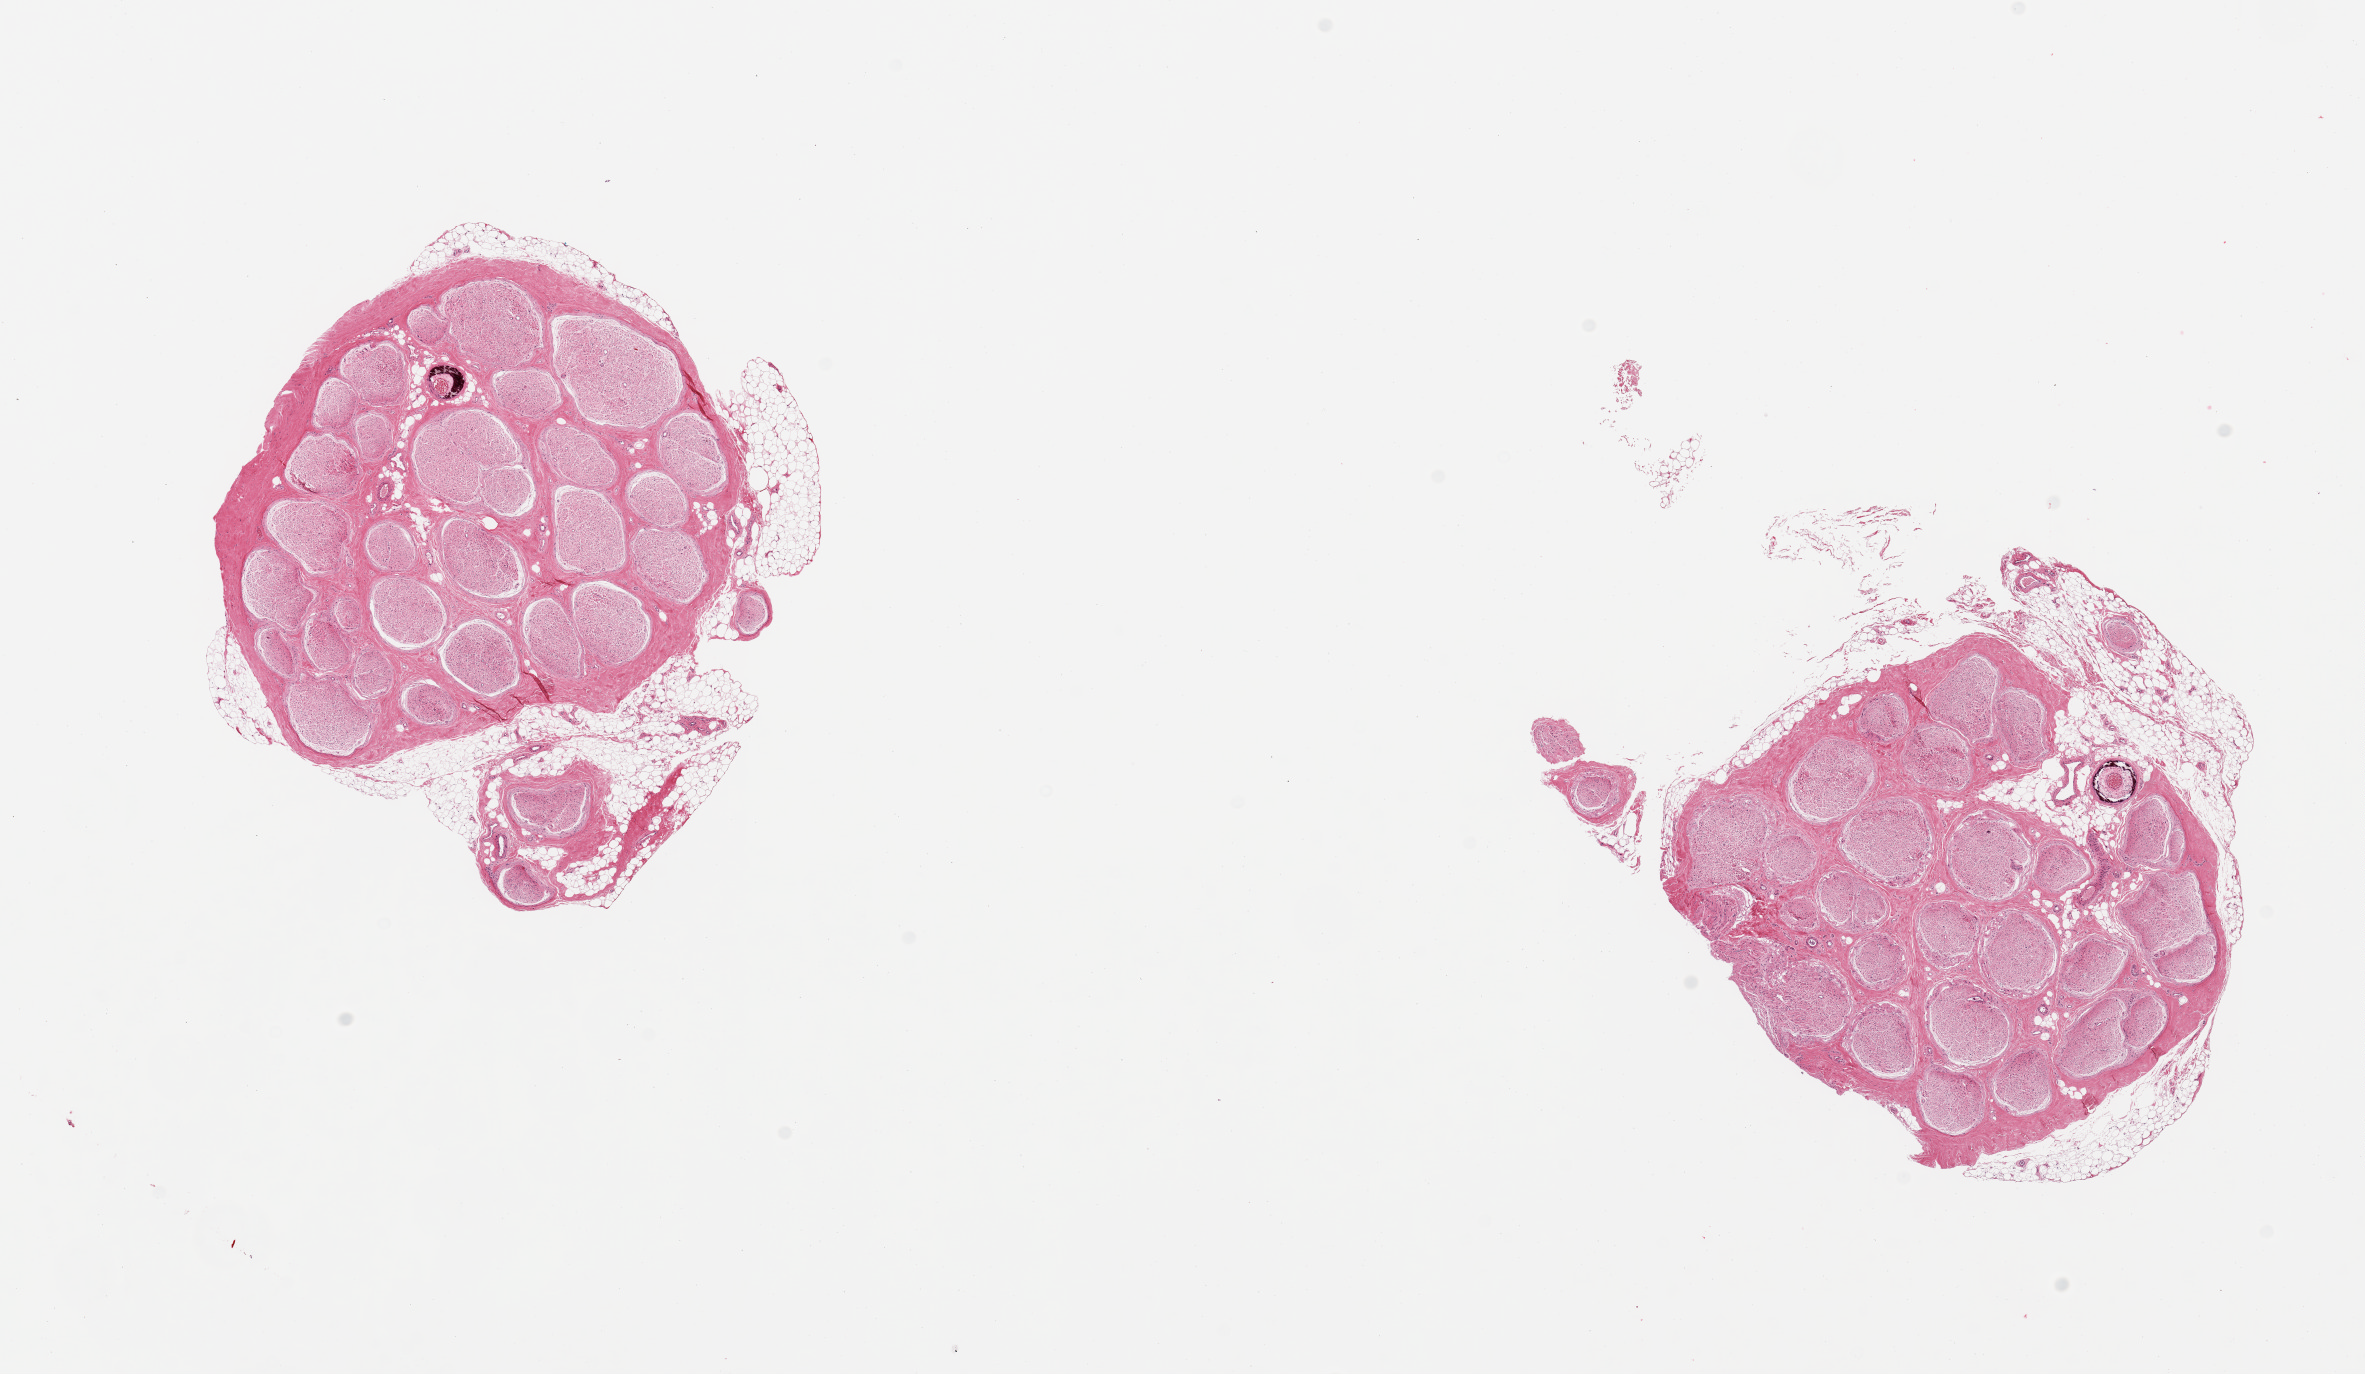
Digitized haematoxylin and eosin-stained section, whole scanned area (about 18.7 x 10.9 mm) shown as a low-resolution overview; PAXgene-fixed, paraffin-embedded tissue; sampled site (target tissue): tibial nerve; donor tissue sample. Donor sex: male.
* pathologist's review note for this sample: 2 pieces; both include ~10% rim of attached fat, medial calcification